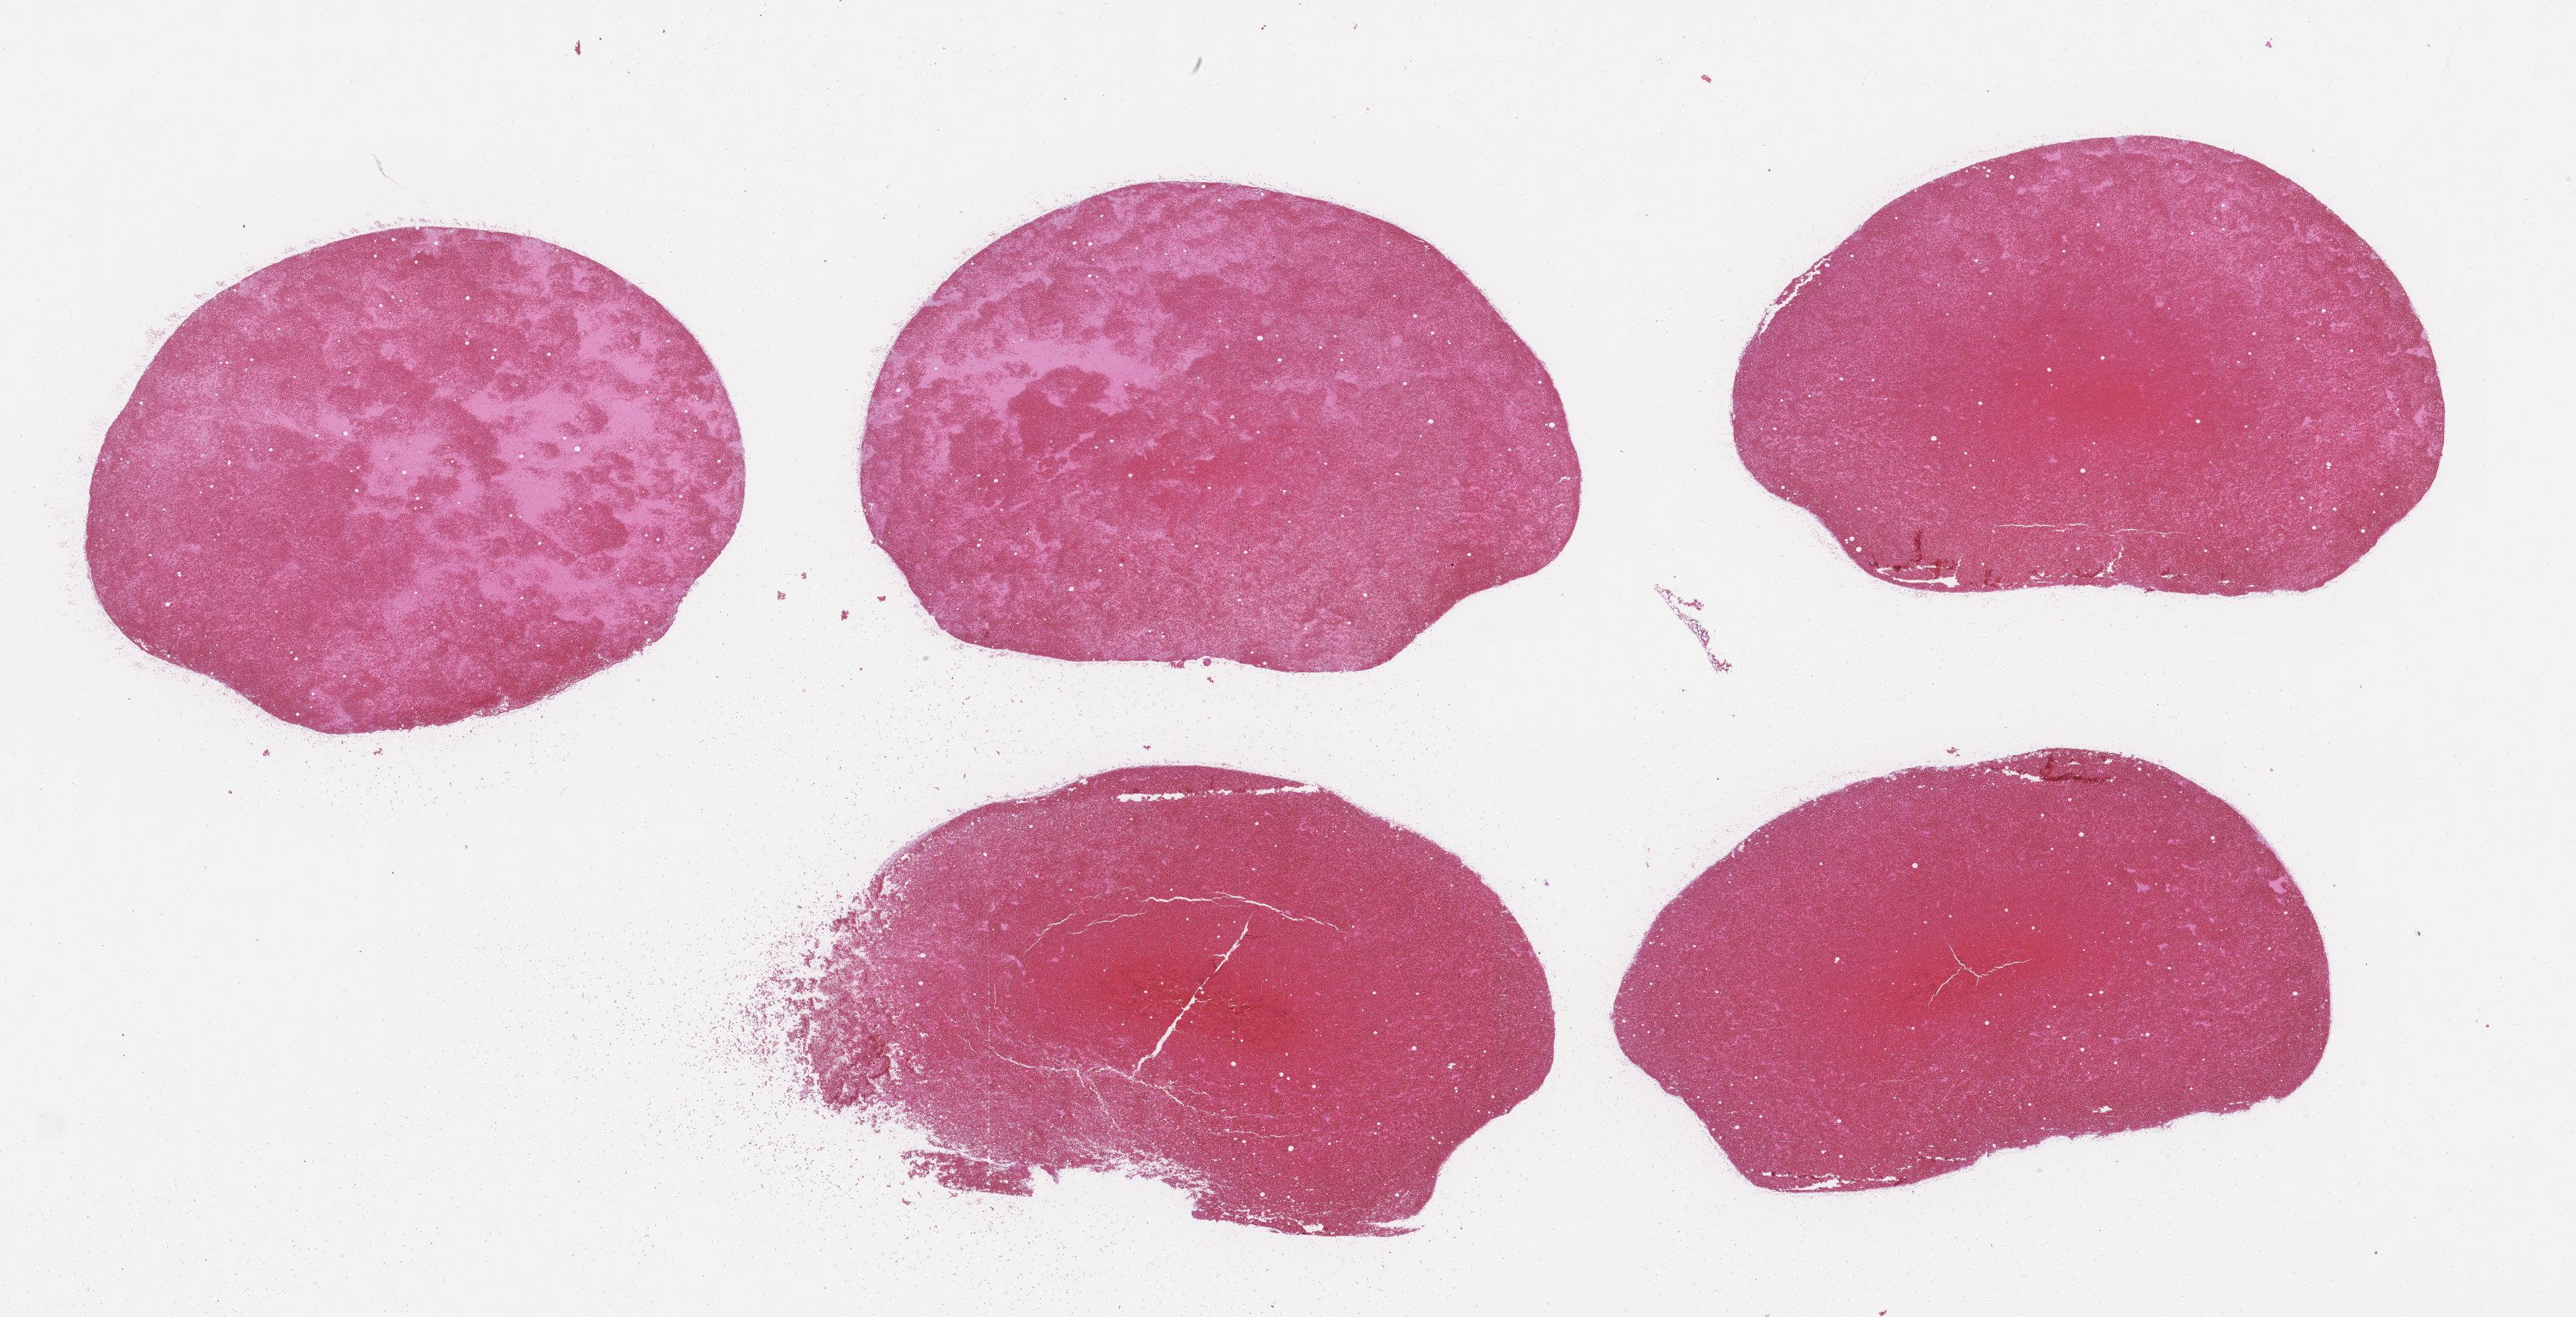
H&E whole-slide image — shown as a low-resolution overview of the whole scanned area (about 29.1 x 14.9 mm); formalin-fixed, paraffin-embedded (FFPE) tissue; site: bone marrow. Patient sex: male.
This section: primary tumour tissue. Diagnosis: Acute Myeloid Leukemia Not Otherwise Specified.